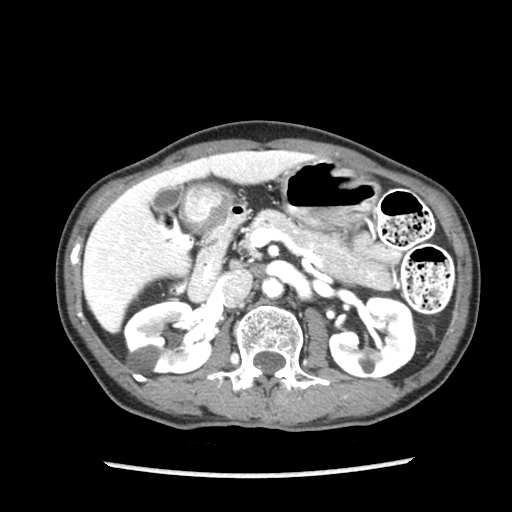
Contrast-enhanced abdominal CT (liver protocol), one axial slice; position 44 of 87 along the scan axis; reconstruction kernel STANDARD; soft-tissue window (W 400 / L 40 HU); 2.5 mm slice thickness; 512 × 512 image matrix, field of view 300 × 300 mm. Case-level facts recorded for this patient, not image findings: diagnosis: hepatocellular carcinoma (patient treated with transarterial chemoembolisation; whether this scan precedes or follows treatment is not stated here); TNM stage (as recorded): Stage-IIIB; Child-Pugh class: A; tumour differentiation: well differentiated; tumour nodularity: uninodular.
Outlined on this slice (semi-automatically segmented with operator editing):
- liver parenchyma outside the tumour (the mass and vessels are separate outlines, so this box may not span the whole liver): bounding box <82,150,317,332> (left, top, right, bottom; pixels)
- liver vessels: <90,165,245,303>